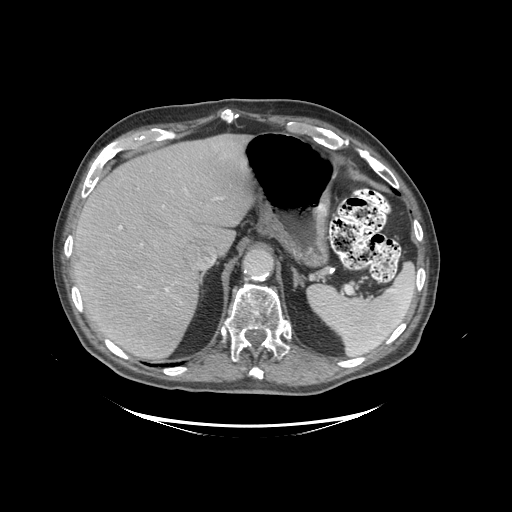
Contrast-enhanced abdominal CT (liver protocol), one axial slice. Position 72 of 99 along the scan axis. 140 kVp. Soft-tissue window (W 400 / L 40 HU). 512 × 512 image matrix, field of view 460 × 460 mm. Case-level facts recorded for this patient, not image findings: diagnosis: hepatocellular carcinoma (patient treated with transarterial chemoembolisation; whether this scan precedes or follows treatment is not stated here); TNM stage (as recorded): Stage-I; Child-Pugh class: A; tumour differentiation: moderately differentiated; tumour nodularity: uninodular.
Annotated regions visible in this slice (semi-automatically segmented with operator editing):
- liver parenchyma outside the tumour (the mass and vessels are separate outlines, so this box may not span the whole liver): bounding box [x1, y1, x2, y2] px = [72, 134, 254, 360]
- liver vessels: [89, 191, 214, 291]